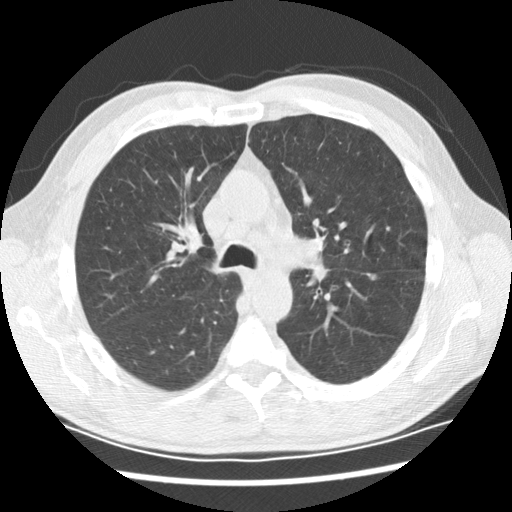
Low-dose screening chest CT, one axial slice; slice 134 of 208 in the series (ordered by position); reconstruction kernel STANDARD; lung window (W 1500 / L -600 HU); 2.5 mm slice thickness; 512 × 512 image matrix.
Structures marked on this image (expert manual segmentation):
- lesion 2 (tumor, lower lobe of left lung): bounding box <366,273,377,281> (left, top, right, bottom; pixels)